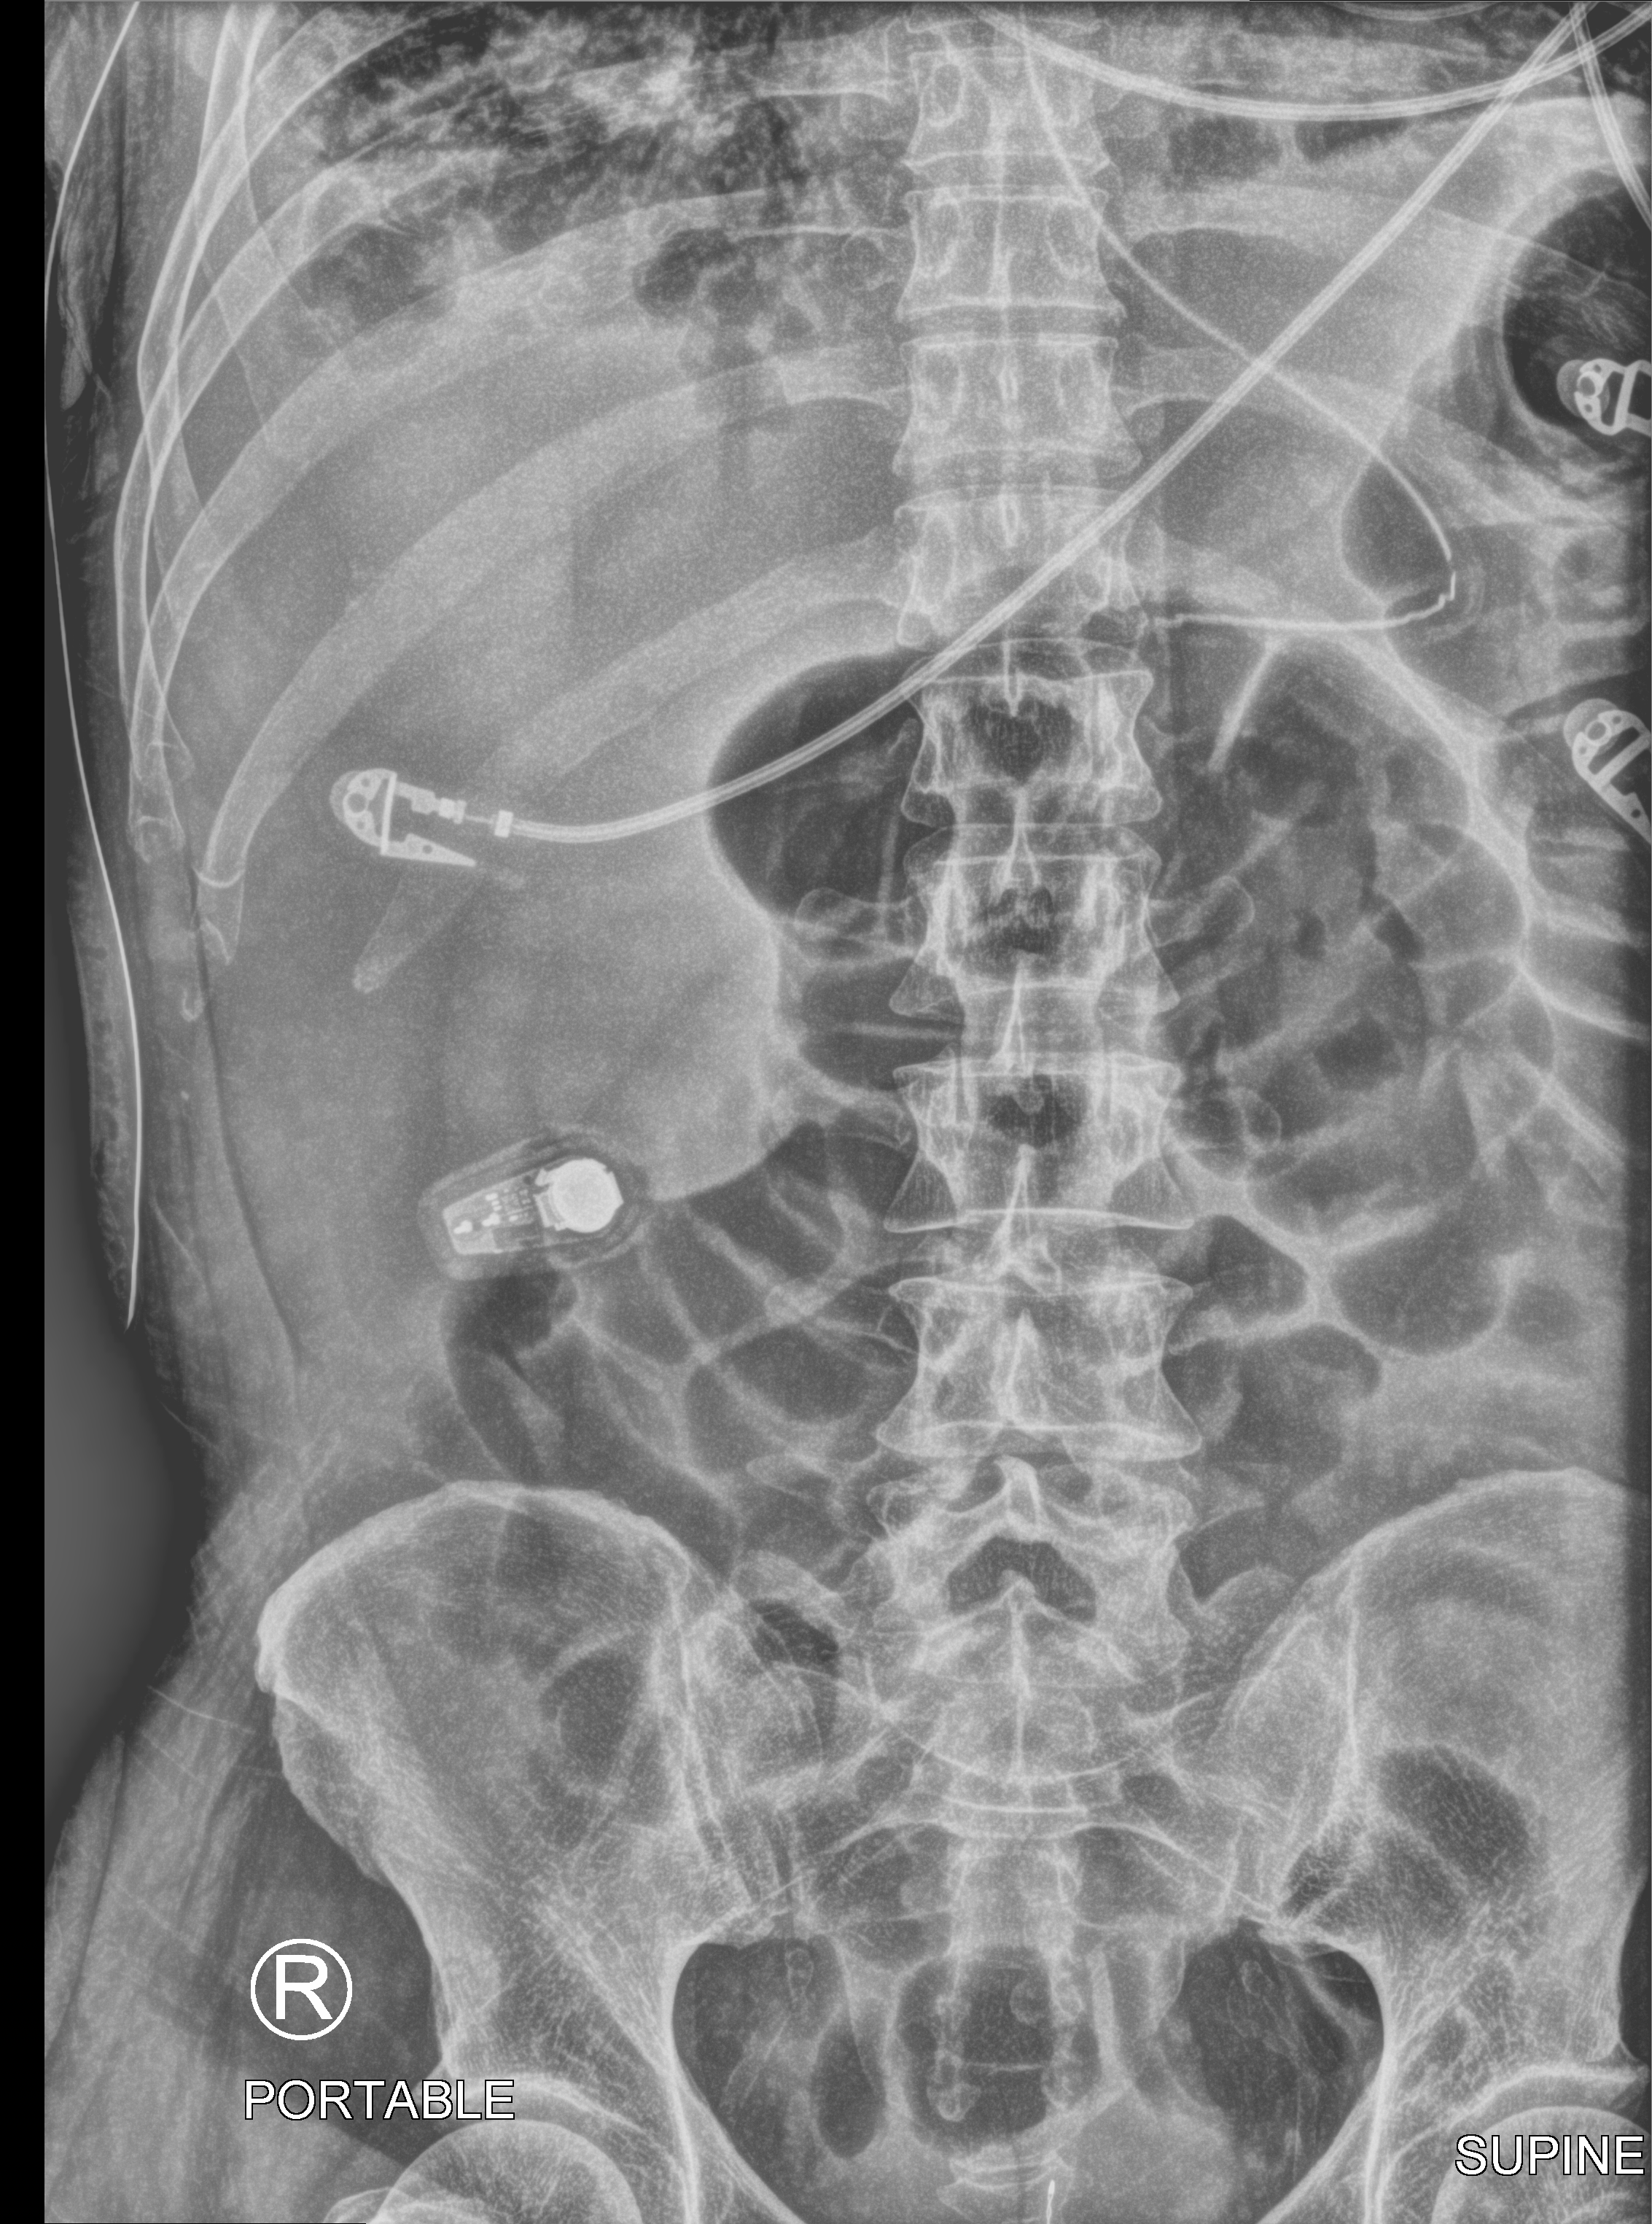
Portable abdomen radiograph; anteroposterior (AP) projection. Patient hospitalised with COVID-19; male, aged 18–59 years.
Admission-level facts for this patient (not findings on this image; timing relative to this image not recorded): admitted to intensive care during this hospital stay: yes.